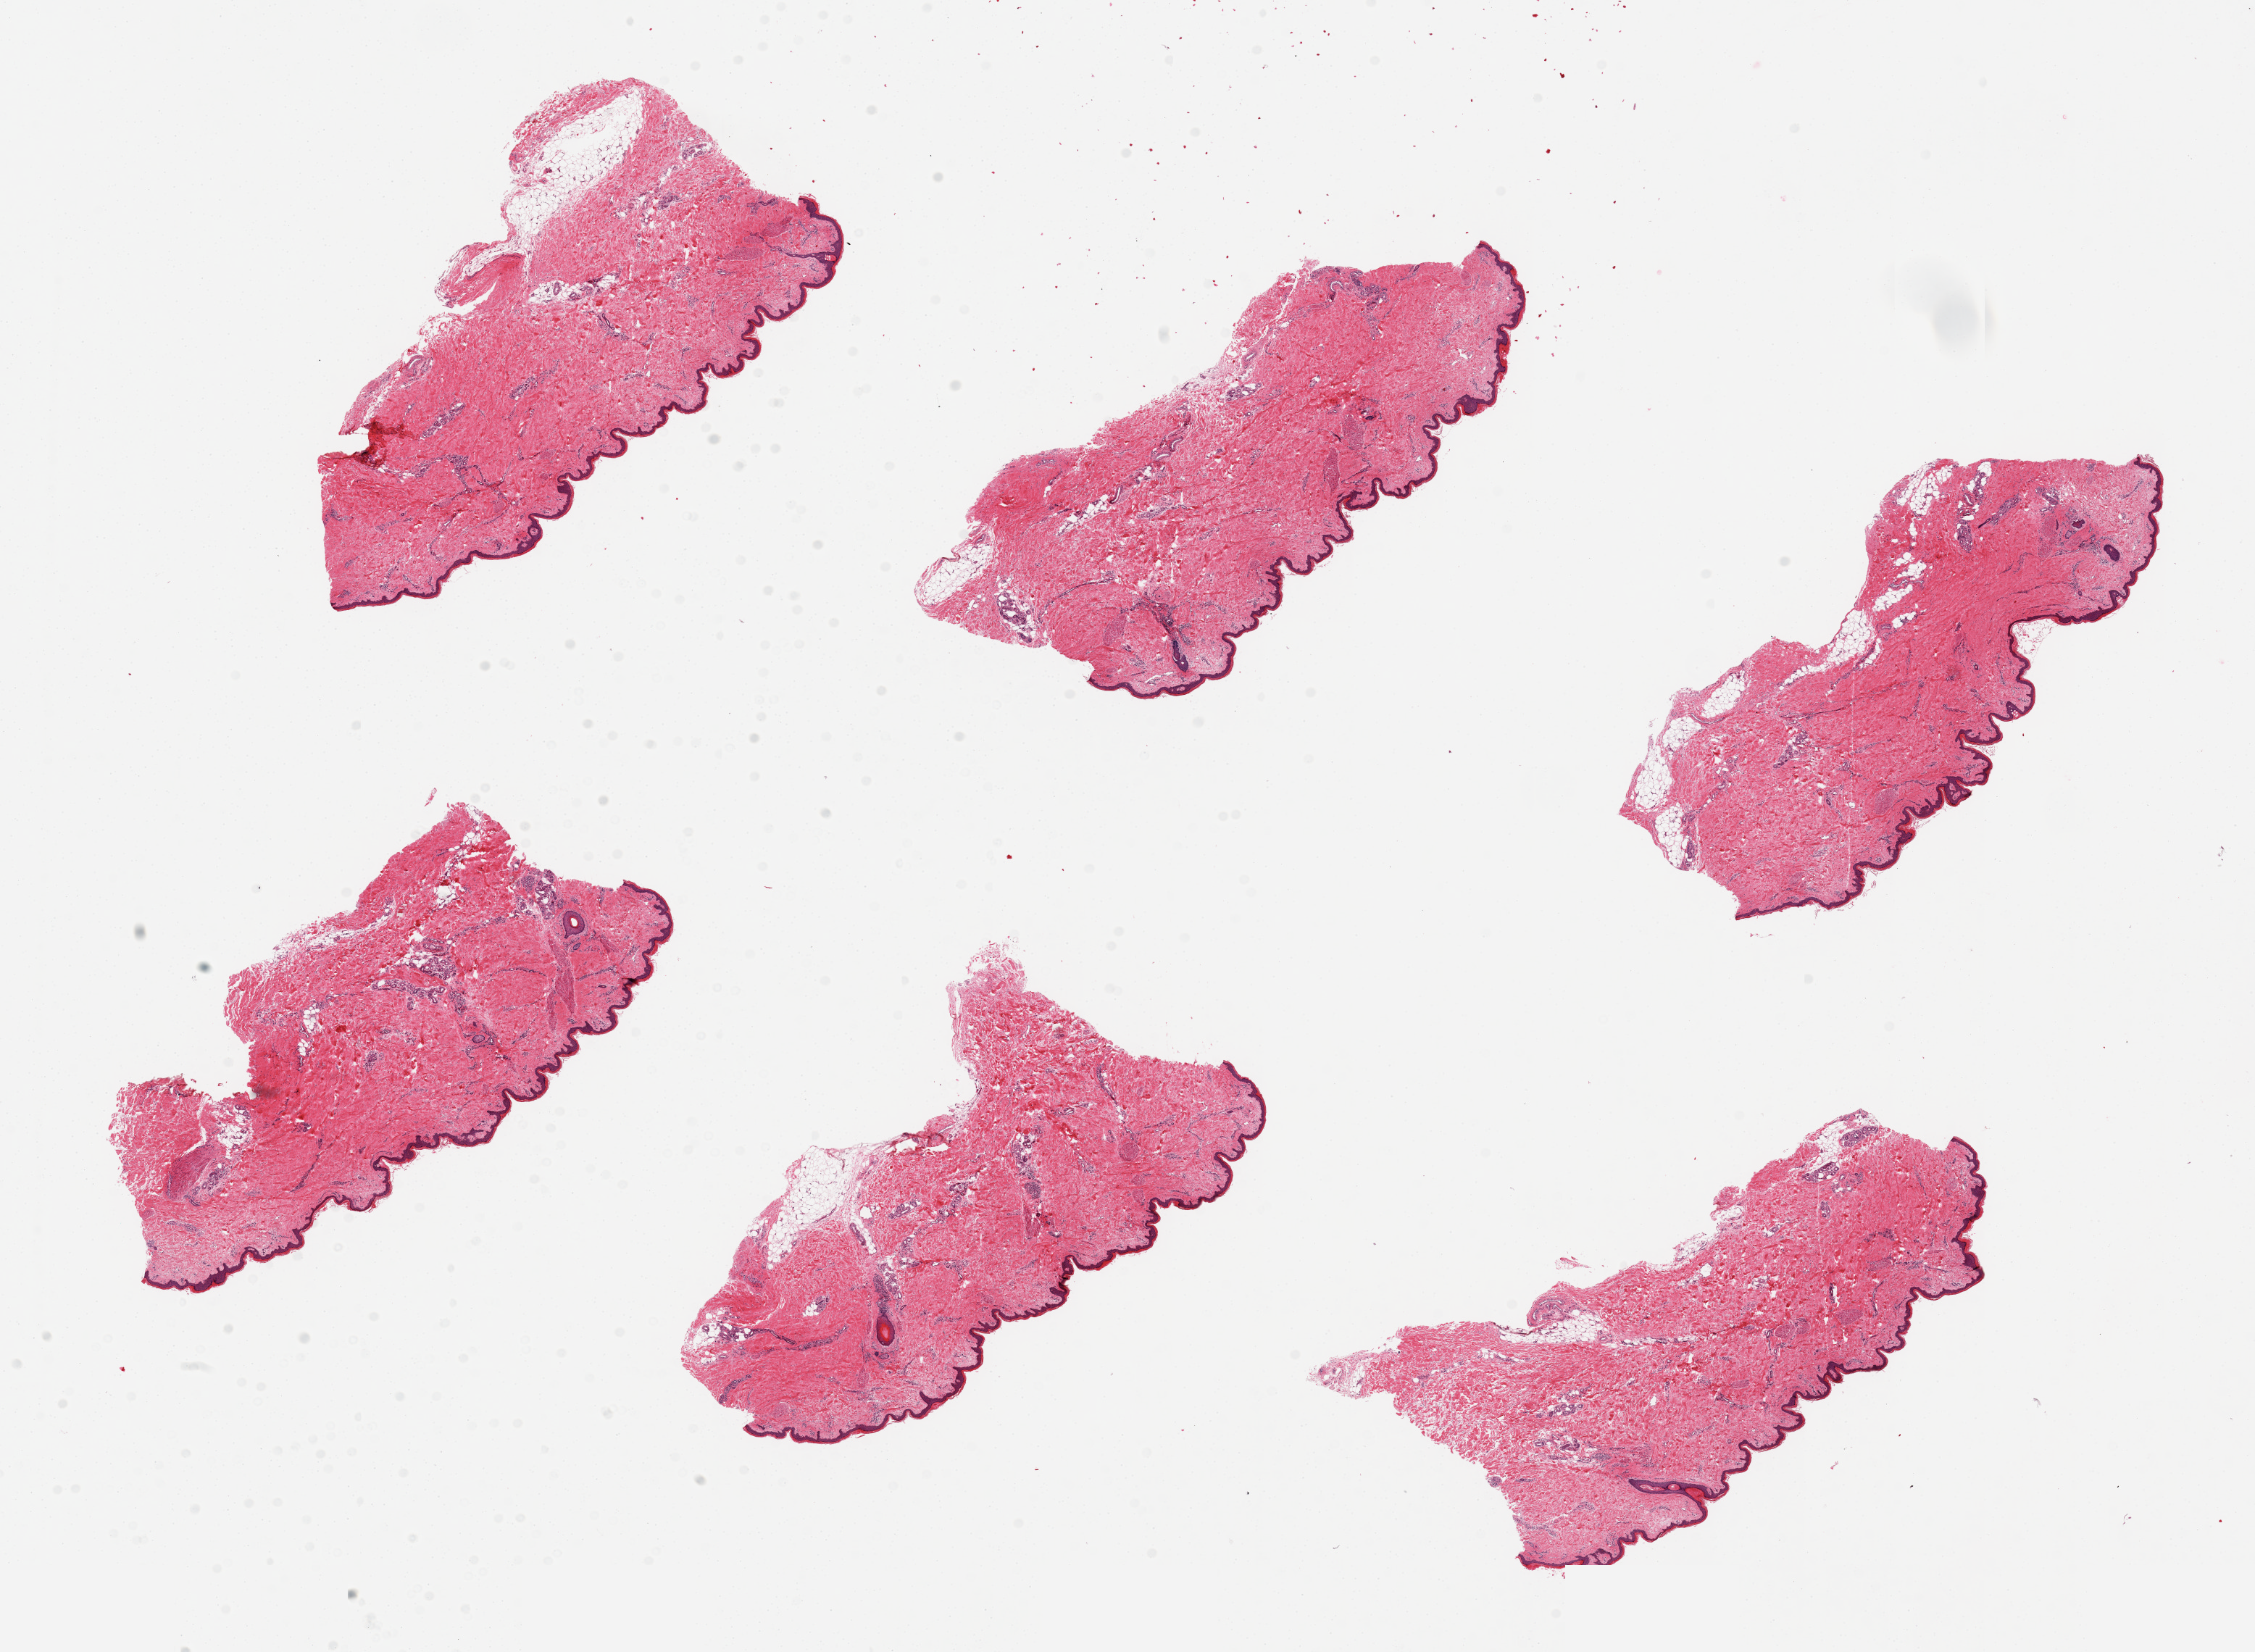
Haematoxylin and eosin whole-slide image, shown as a low-resolution overview of the whole scanned area (about 24.6 x 18.0 mm, slide scanned at 20x); PAXgene-fixed paraffin-embedded (PFPE) section; sampled site (target tissue): skin of lower leg; donor tissue sample. Male donor.
• review note (as recorded): 6 pieces. Well trimmed